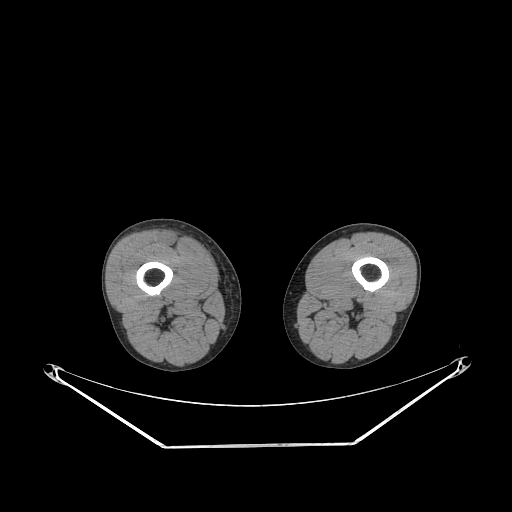
CT of an extremity soft-tissue mass (from a PET/CT study), one axial slice; slice 225 of 311 in the series (ordered by position); reconstruction kernel STANDARD; soft-tissue window (W 400 / L 40 HU); 3.75 mm slice thickness; 512 × 512 image matrix, field of view 500 × 500 mm. Male patient. Case-level facts recorded for this patient, not image findings: histological type: pleiomorphic leiomyosarcoma; grade: intermediate; site of the primary tumour: right thigh.
Outlined on this slice (expert contour drawn on MRI and transferred to this co-registered scan by the dataset authors):
- gross tumour volume including surrounding oedema: bounding box <164,235,181,247> (left, top, right, bottom; pixels)